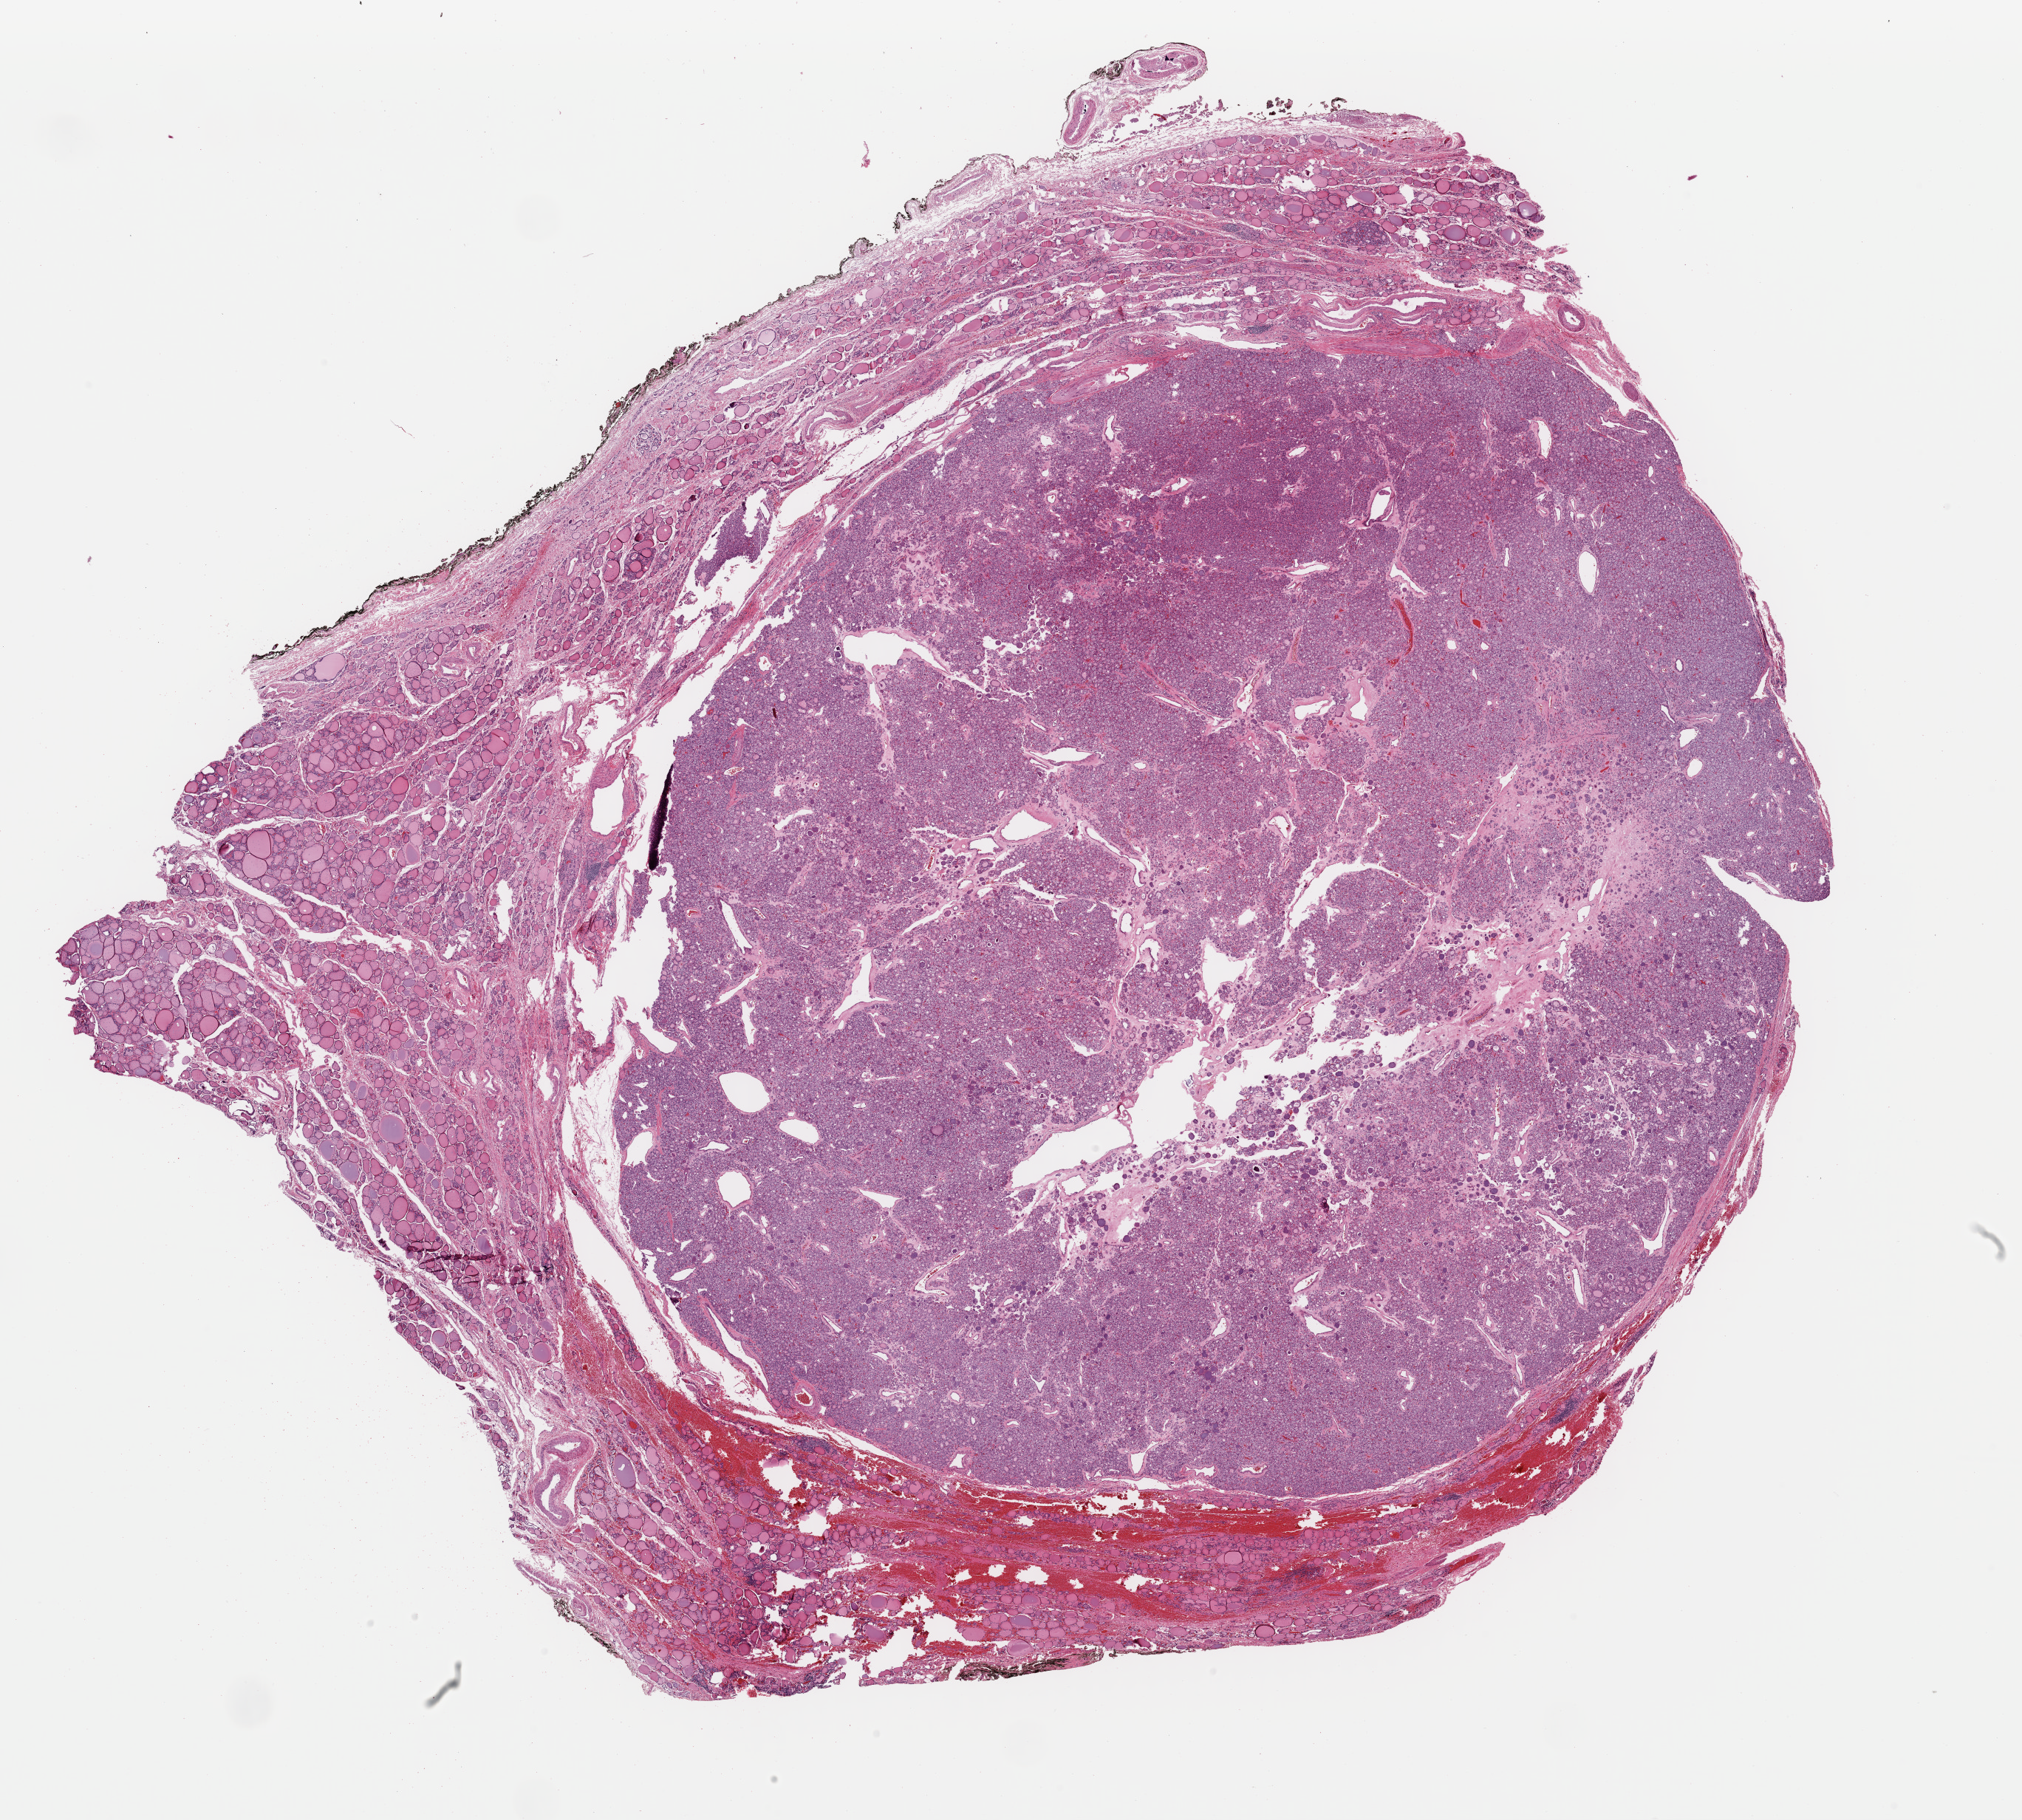
H&E-stained whole-slide image — a low-resolution overview of the entire scanned area, about 21.6 x 19.5 mm (from a 40x scan); formalin-fixed paraffin-embedded (FFPE) diagnostic section; sample: primary tumour, thyroid. Female, age 64 years at initial diagnosis.
* AJCC pathologic stage: I (7th edition)
* histologic diagnosis: Papillary adenocarcinoma, NOS (thyroid gland)